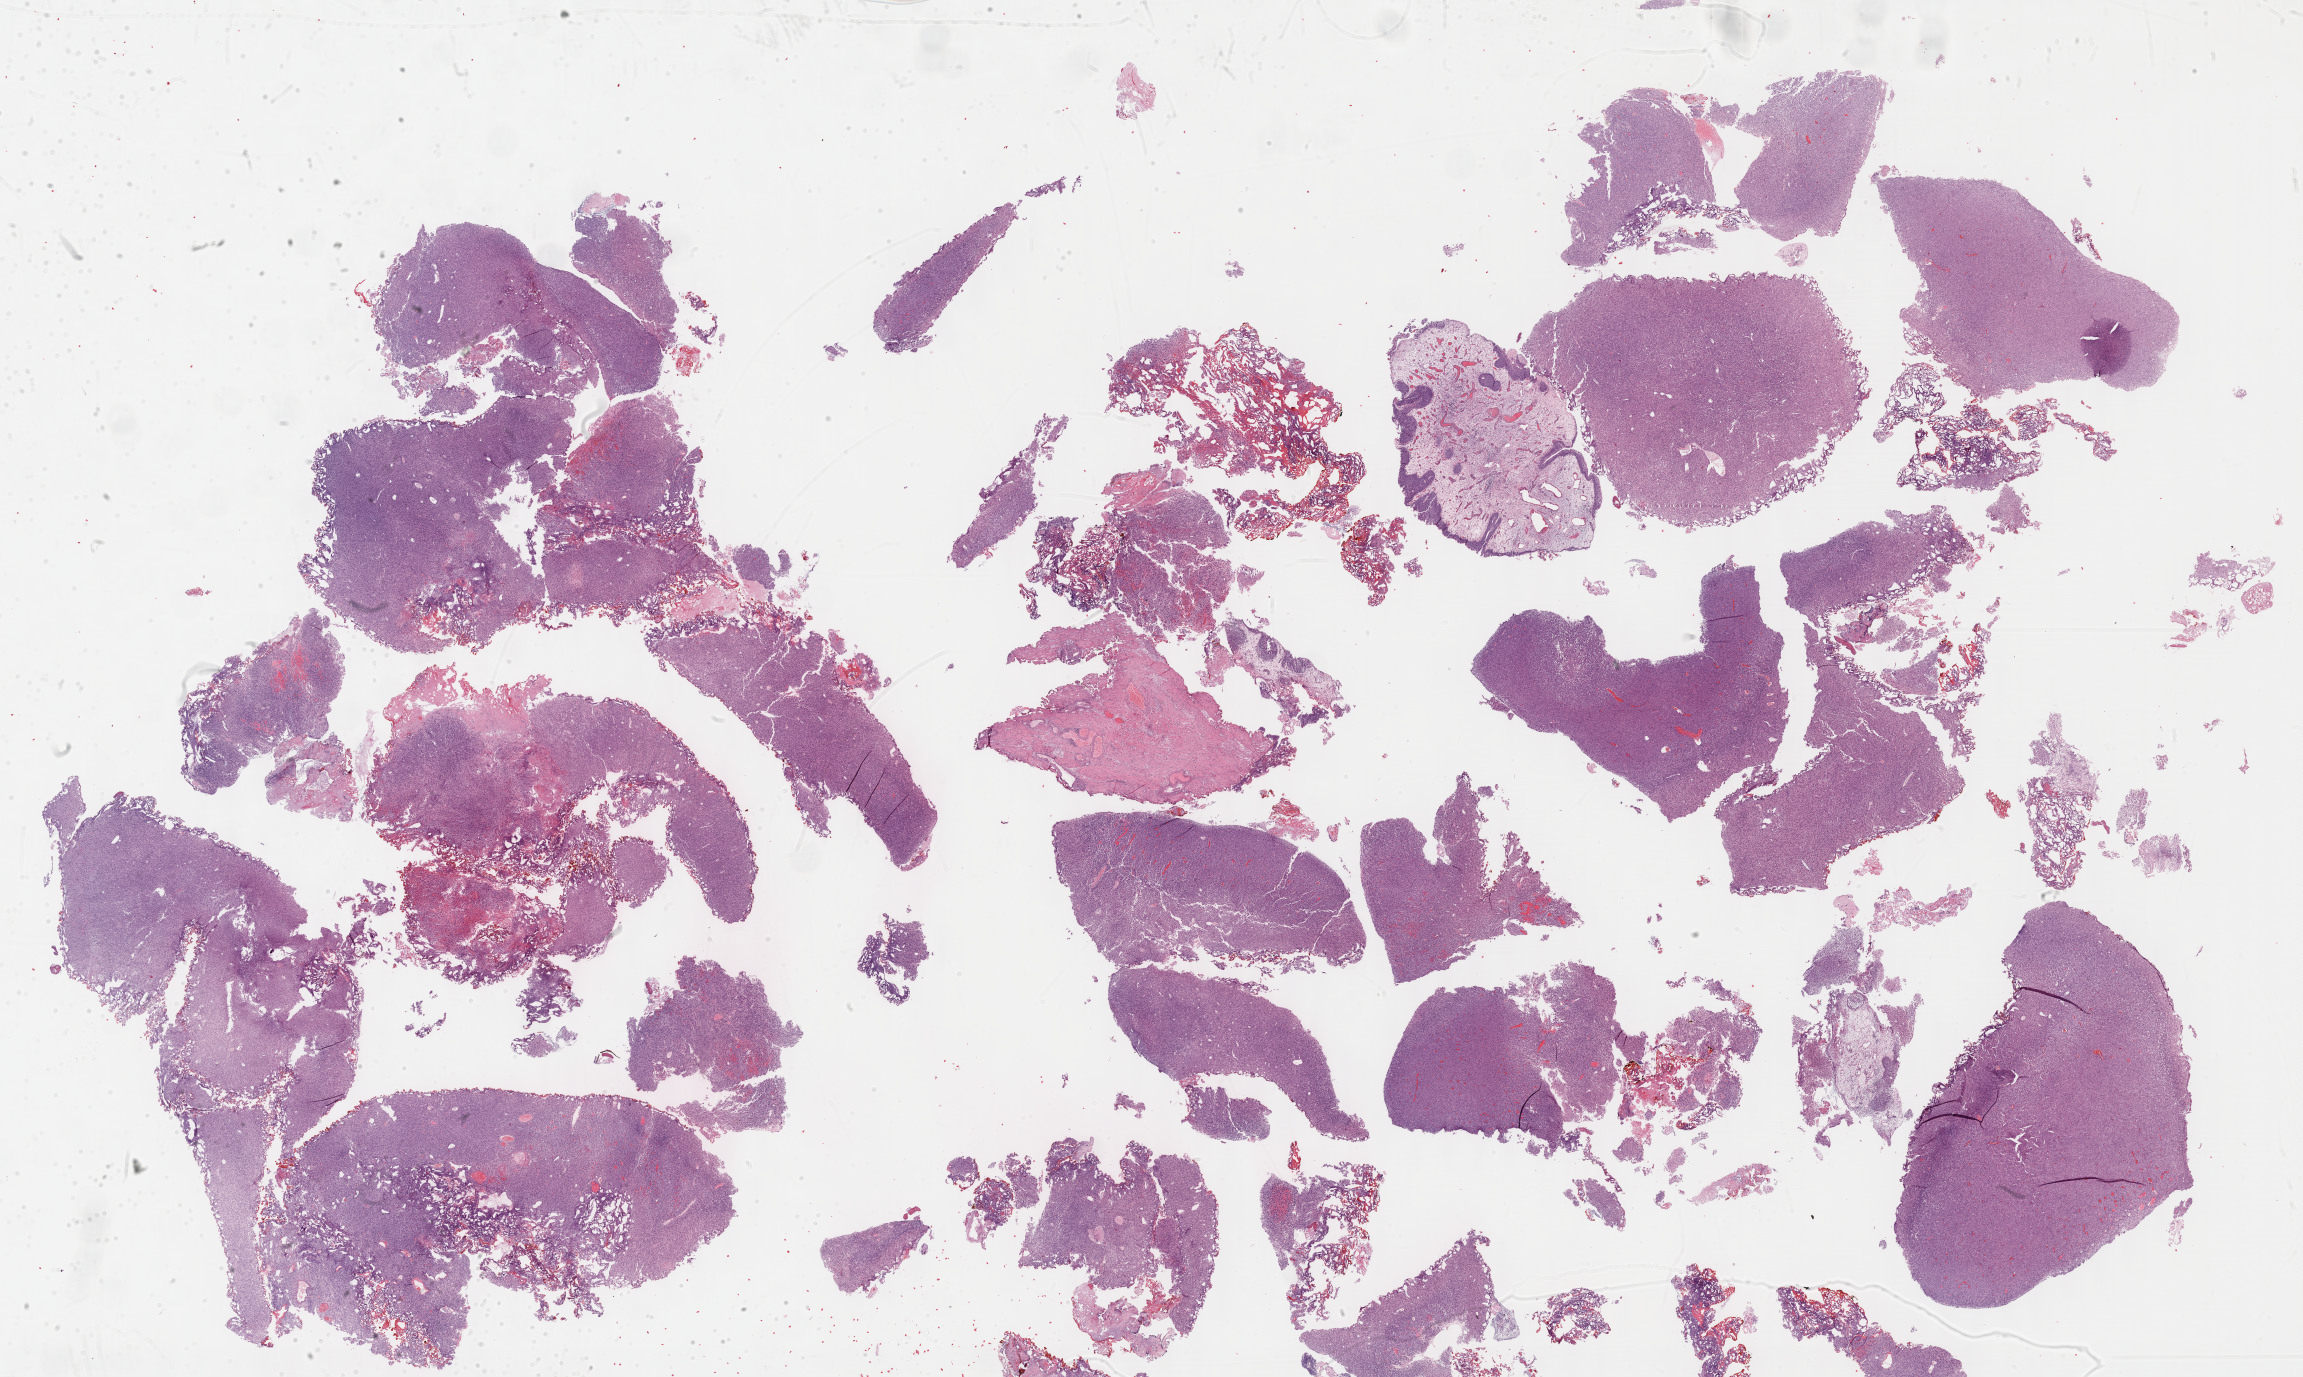
H&E-stained whole-slide image — shown as a low-resolution overview of the whole scanned area (about 37.2 x 22.3 mm, slide scanned at 40x); formalin-fixed paraffin-embedded (FFPE) diagnostic section; sample: primary tumour, bladder. Patient: male, age at initial diagnosis 66 years. Histologic grade: high grade.
Histologic diagnosis: Transitional cell carcinoma. AJCC pathologic stage: IV (6th edition).